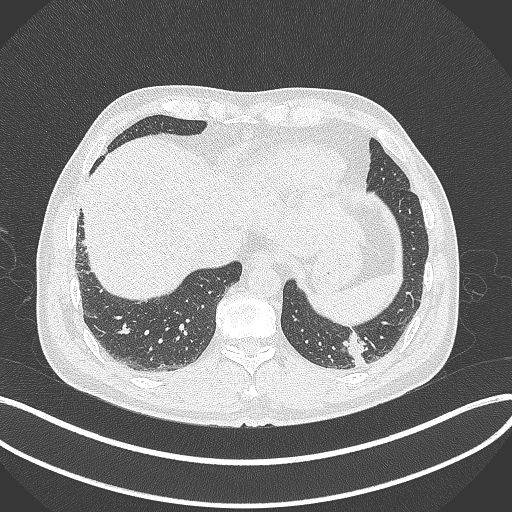
Chest CT, one axial slice. Position 55 of 300 along the scan axis. Reconstruction kernel B70f. 120 kVp. Lung window (W 1500 / L -600 HU). 1 mm slice thickness. 512 × 512 image matrix. Patient: male, 54 years. Case-level facts recorded for this patient, not image findings: clinical TNM (as recorded): T1c N0 M1.
Annotated regions visible in this slice (rectangle marked by the reading radiologist):
- lung tumour (recorded histology: adenocarcinoma): bounding box [x1, y1, x2, y2] px = [344, 325, 366, 363]